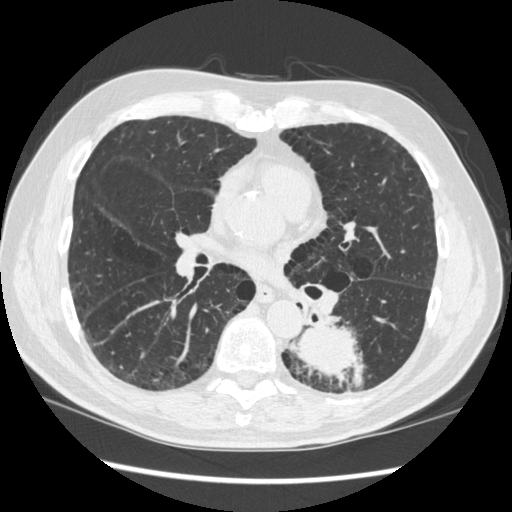
Low-dose screening chest CT, one axial slice; slice 162 of 348 in the series (ordered by position); reconstruction kernel STANDARD; lung window (W 1500 / L -600 HU); 1.25 mm slice thickness; 512 × 512 image matrix, field of view 360 × 360 mm.
Outlined on this slice (expert manual segmentation):
- lesion 1 (tumor, lower lobe of left lung): bounding box [x1, y1, x2, y2] px = [289, 323, 365, 390]